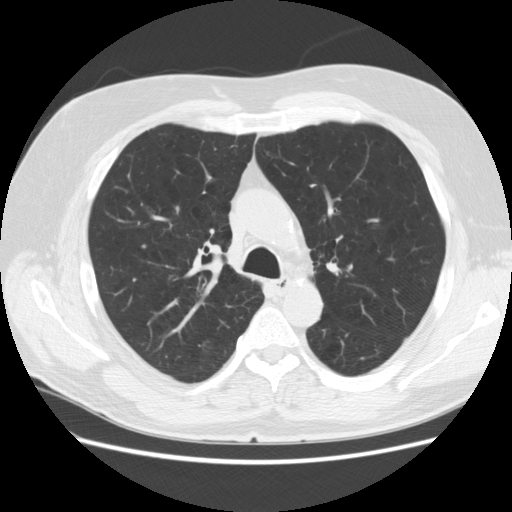
Low-dose screening chest CT, axial slice; first (baseline) screen; lung window (W 1500 / L -600 HU); 2.5 mm slice thickness; 120 kVp; slice 63 of 186 in the series; 512 × 512 image matrix. Male, age 63 years at enrolment. Former smoker at enrolment.
Expert-annotated lung lesion, bounding box (x1, y1, x2, y2) in pixels: (158, 195, 195, 223). No non-calcified nodule or mass ≥4 mm was recorded by the screening reader at this exam. Official screen result: negative screen, minor abnormalities not suspicious for lung cancer.